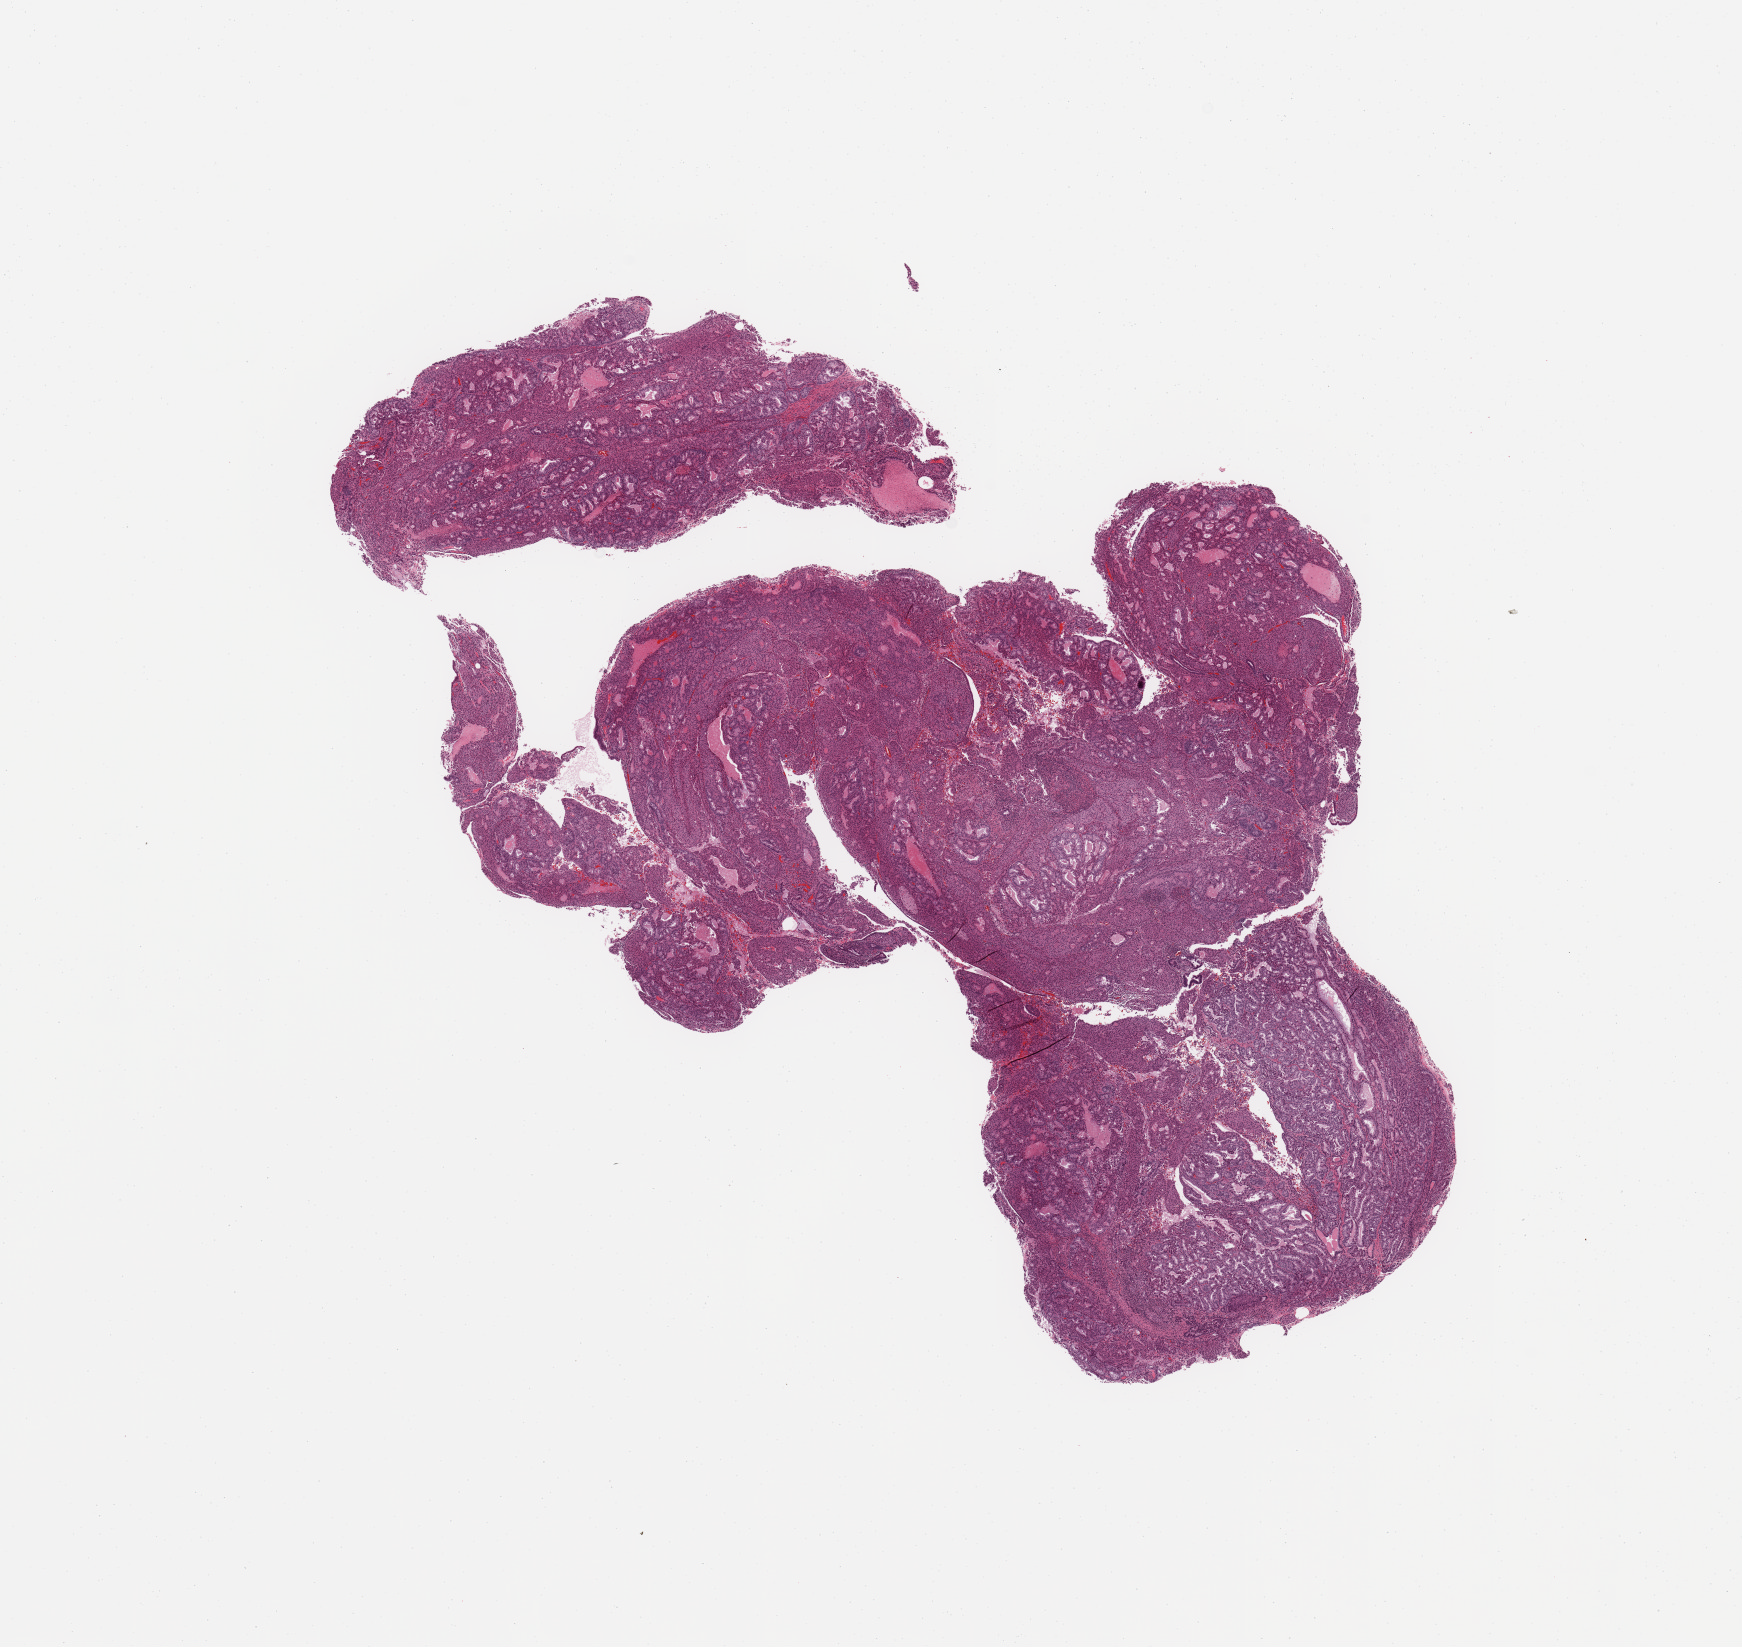
Digitized Hematoxylin and eosin (H&E) stained tissue section (whole slide) — low-resolution overview of the scanned area, about 13.8 x 13.0 mm (slide scanned at 20x). Tumour tissue sample, sampled site: uterus. Female, 68 y/o. Histologic grade: G1 (well differentiated). Composition of this section per pathologist review: tumour nuclei 90%, necrosis 5%.
• diagnosis: Endometrioid adenocarcinoma, NOS
• AJCC pathologic stage: I